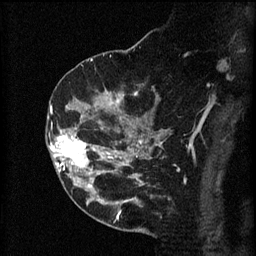
Breast MRI (dynamic contrast-enhanced), one sagittal slice. Slice 36 of 60 in the series (ordered by position). 3 images stored at this slice position (order not interpretable as contrast timing). 1.5 T. TE 4.2 ms, TR 8.2 ms. 2 mm slice thickness. 256 × 256 image matrix, field of view 180 × 180 mm. Female patient, age 49 years.
Structures marked on this image (semi-automatic segmentation, software-assisted and operator-edited):
- analysis volume of interest (the breast-tissue region the enhancement analysis was run in; not a lesion): box from (x=46, y=126) to (x=105, y=177) px
- tumour enhancement mask (voxels above the 70 % enhancement threshold inside the analysis volume of interest): (x=49, y=130)–(x=104, y=175)